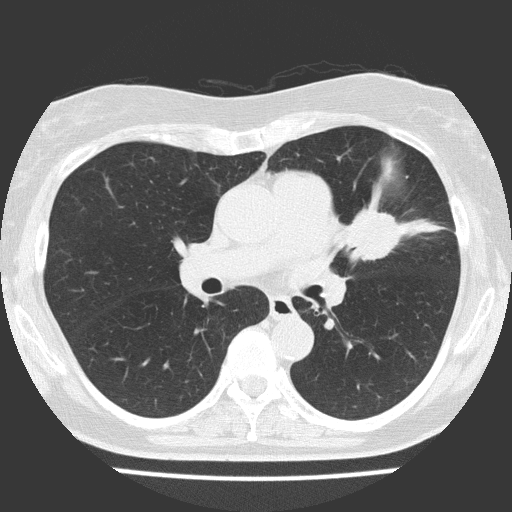
Low-dose screening chest CT, axial slice. Baseline screening round. Lung window (W 1500 / L -600 HU). 2 mm slice thickness. Lung (sharp) reconstruction kernel (FC51). 120 kVp. Female participant, aged 70 years at enrolment.
Lesion marked by an expert reader, box from (x=323, y=184) to (x=432, y=277) px. The screening reader recorded 2 non-calcified nodules or masses ≥4 mm on this exam; which of them this box marks is not recorded. Later outcome: lung cancer diagnosed 25 days after this screen — adenocarcinoma, NOS, left upper lobe, poorly differentiated (G3), stage IV (AJCC 6th edition), 30 mm at pathology.